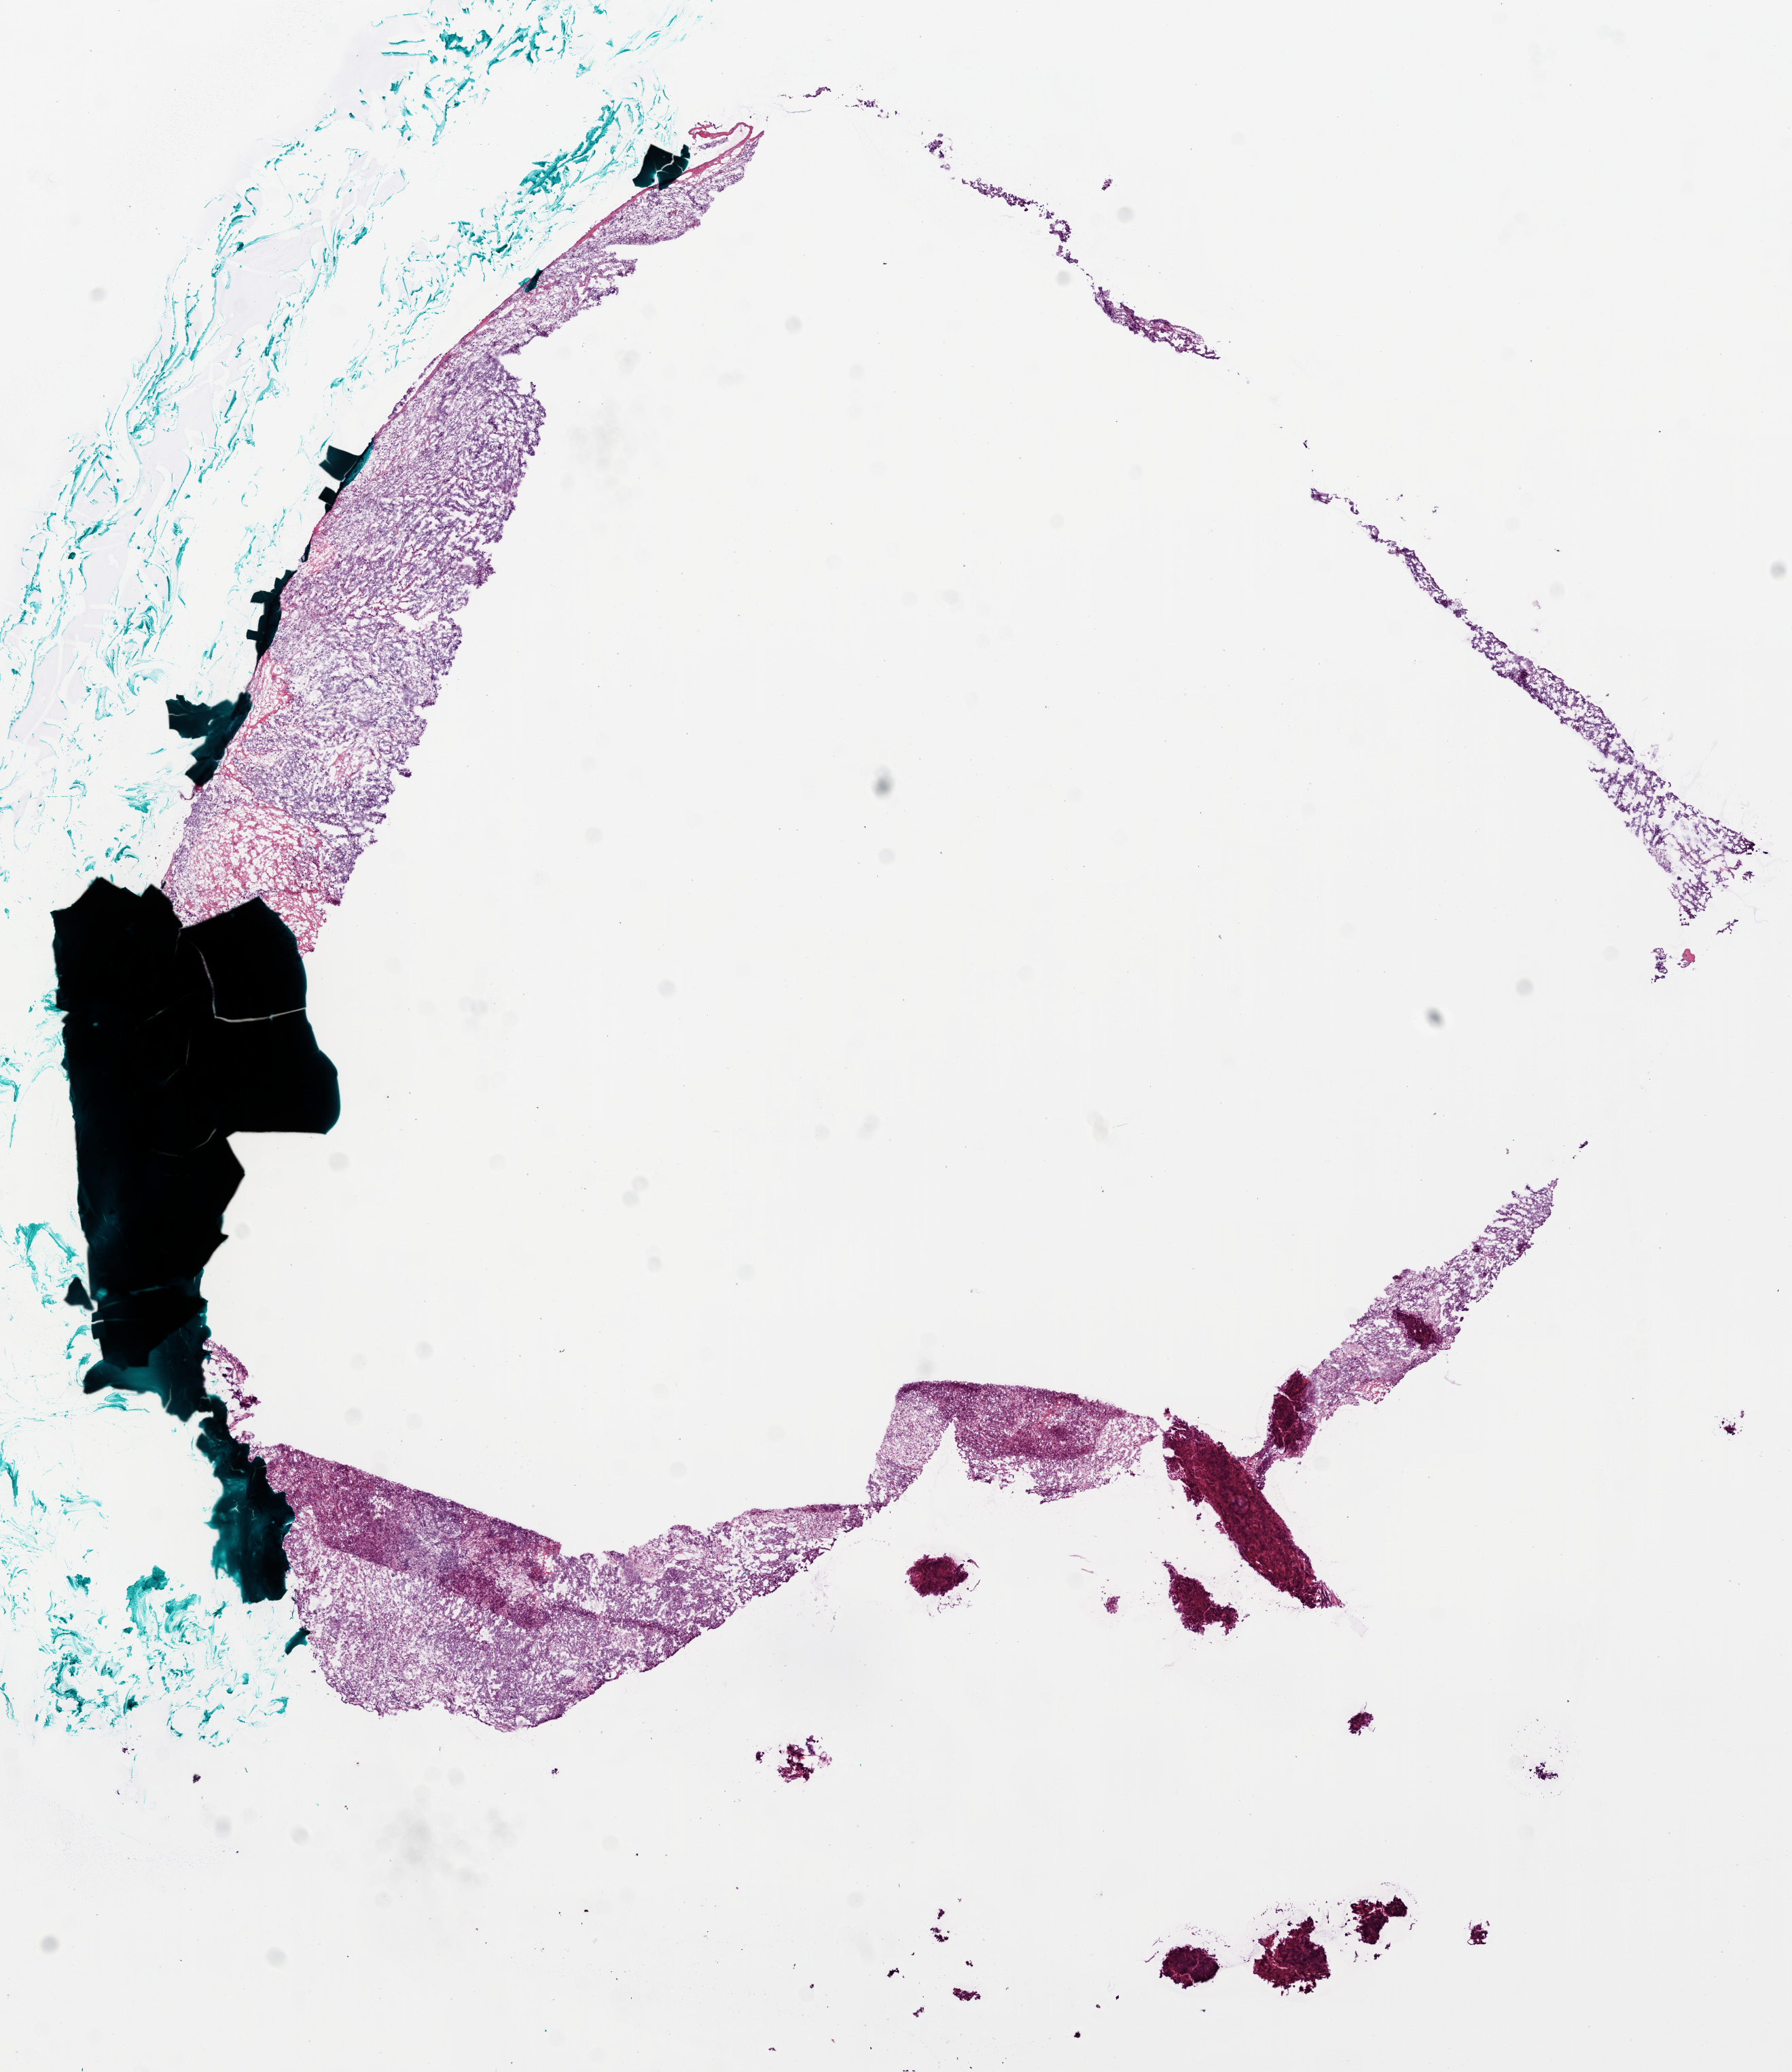
Digitized H&E tissue section (whole slide) — shown as a low-resolution overview of the whole scanned area (about 10.6 x 12.3 mm). Frozen section from the bottom of the tissue portion. Sample: primary tumour, ovary. Female, age 71 years at initial diagnosis. Histologic grade: G3 (poorly differentiated). Pathologist review of this section (percent, as recorded): tumour cells 75%, tumour nuclei 85%, normal cells 10%, stromal cells 5%, necrosis 10%. Infiltration values recorded for this section: lymphocyte infiltration 90%.
Laterality: bilateral. Diagnosis: Serous cystadenocarcinoma, NOS. FIGO stage: IIIC.